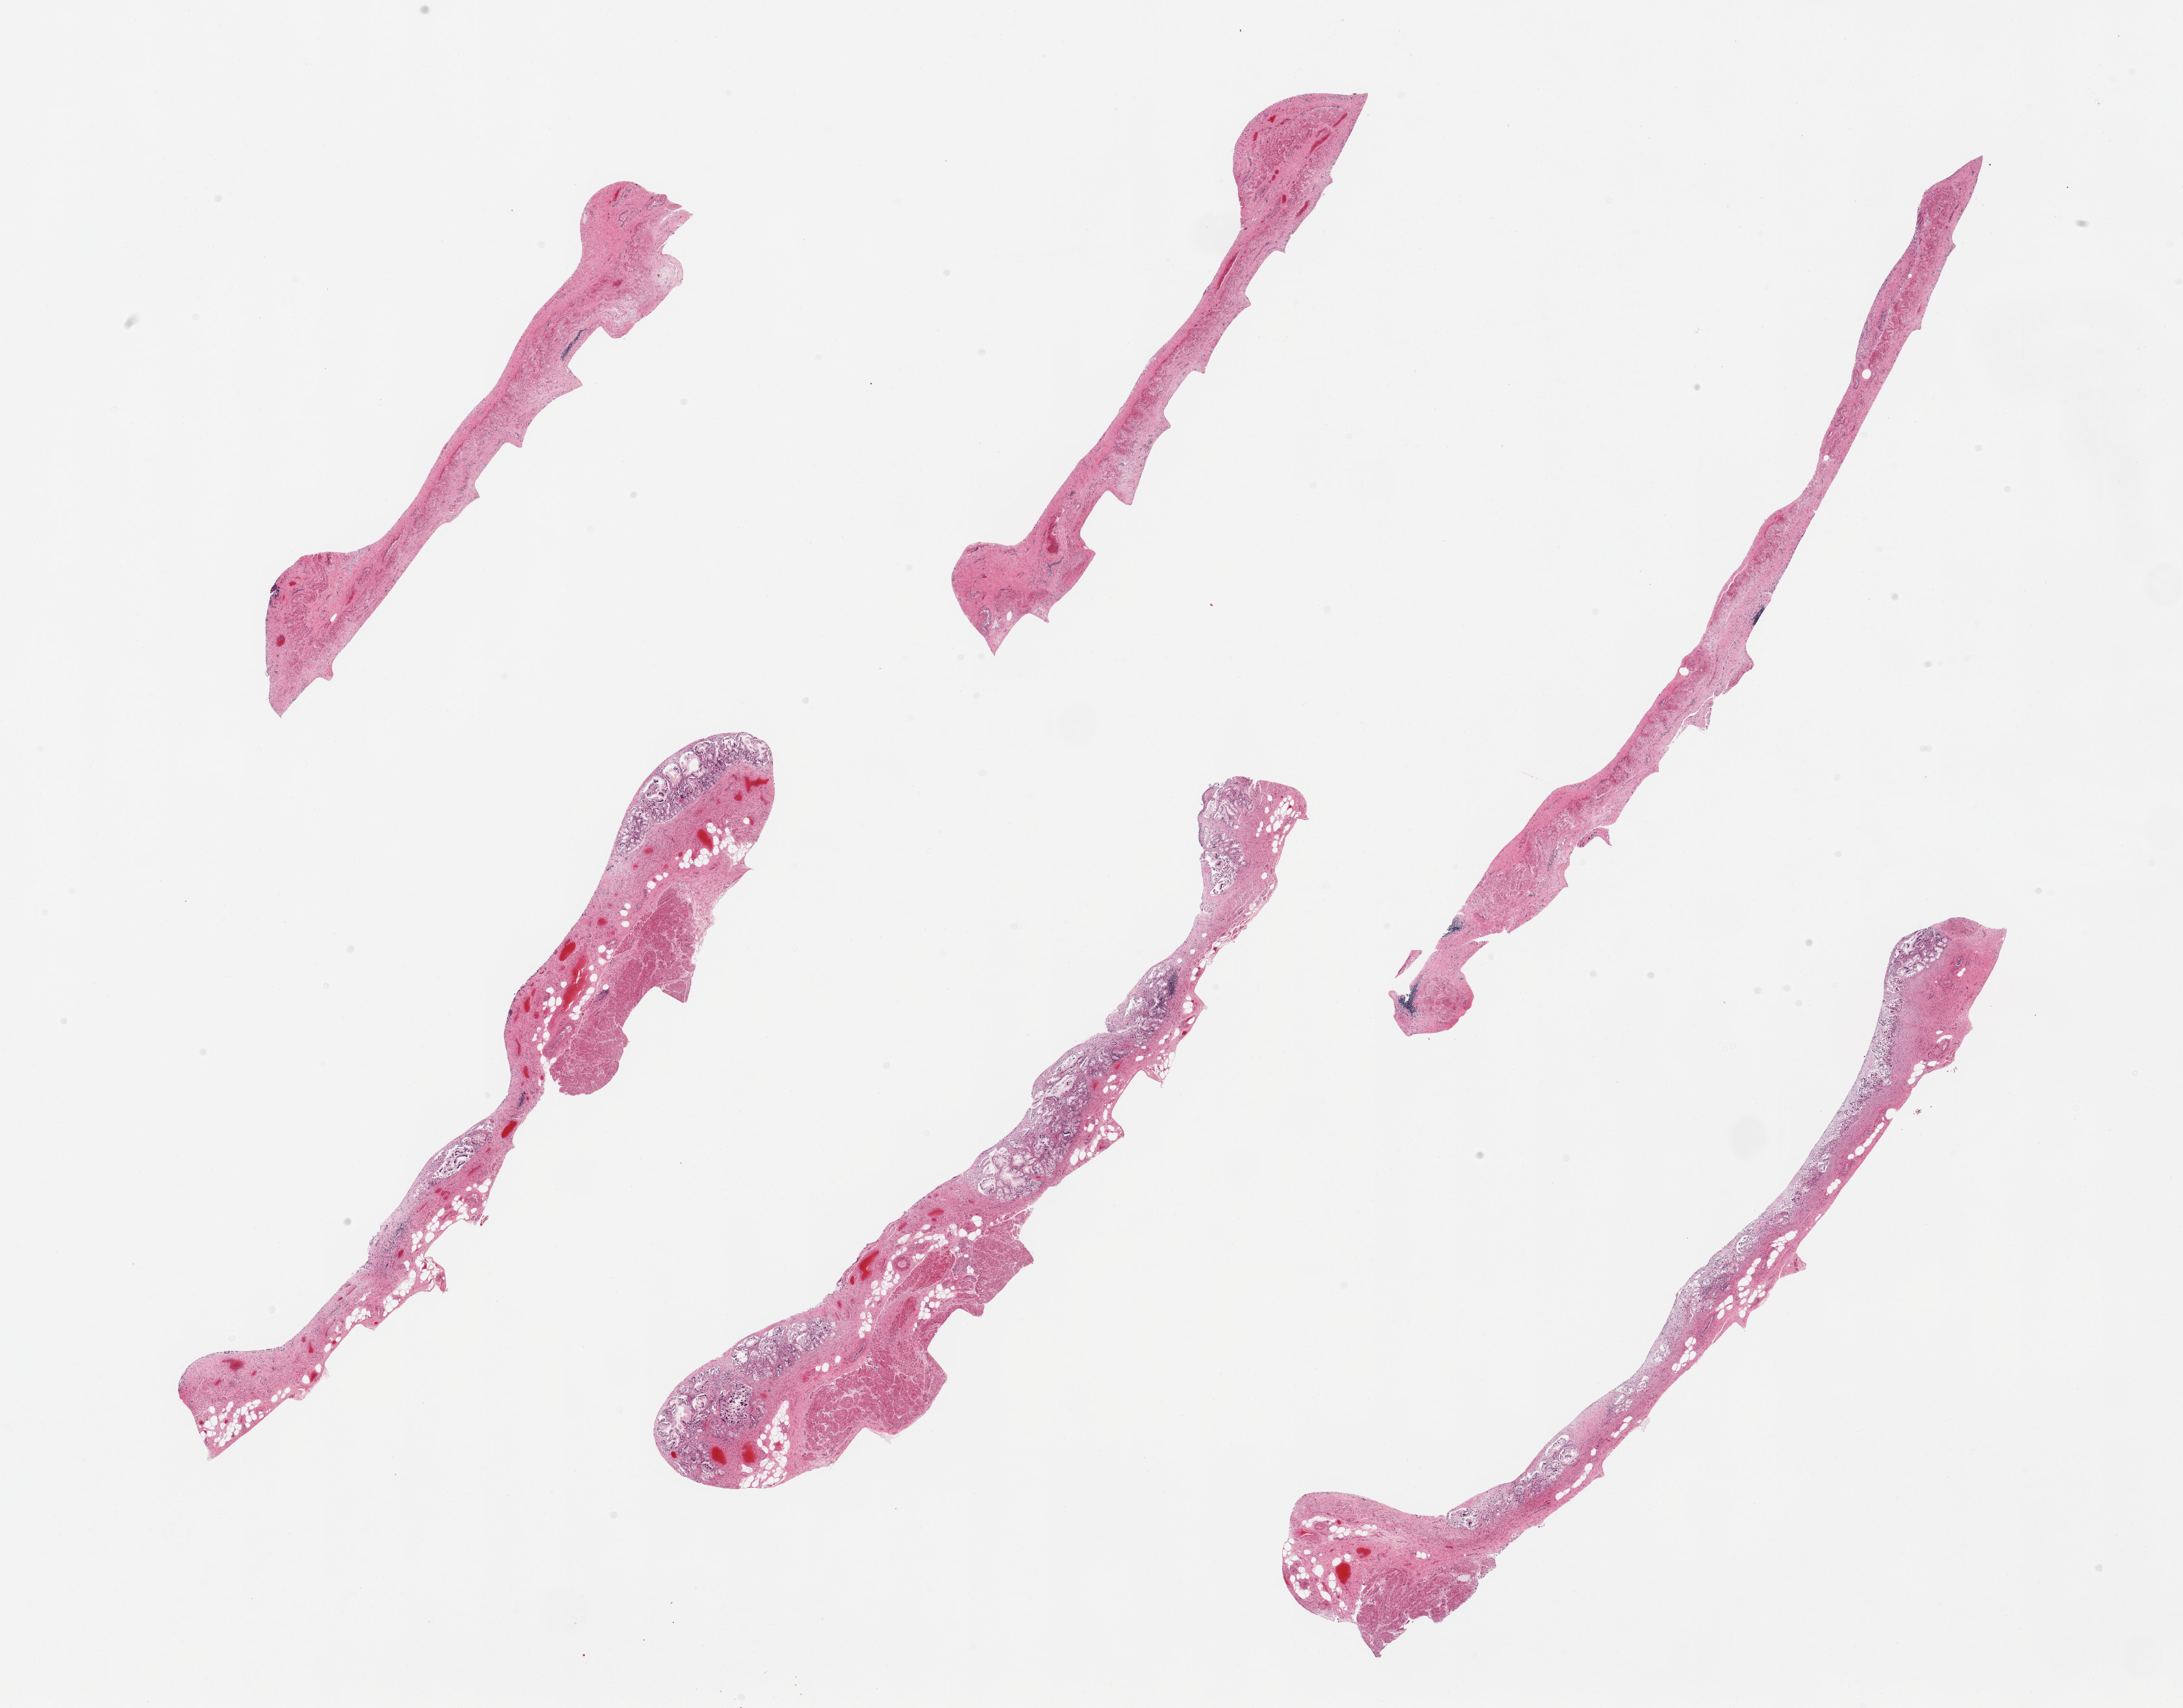
Digitized hematoxylin and eosin (H&E)-stained section, brightfield — shown as a low-resolution overview of the whole scanned area (about 26.6 x 20.8 mm, acquisition: 20x scan); PAXgene-fixed paraffin-embedded (PFPE) section; sampled site (target tissue): esophageal mucous membrane; tissue donor sample. Male donor.
Reviewer comment on this tissue sample: 6 pieces; autolysed grade 3 gastric mucosa and congested muscularis and submucosa; esophageal mucosa (squamous epithelium) not present.